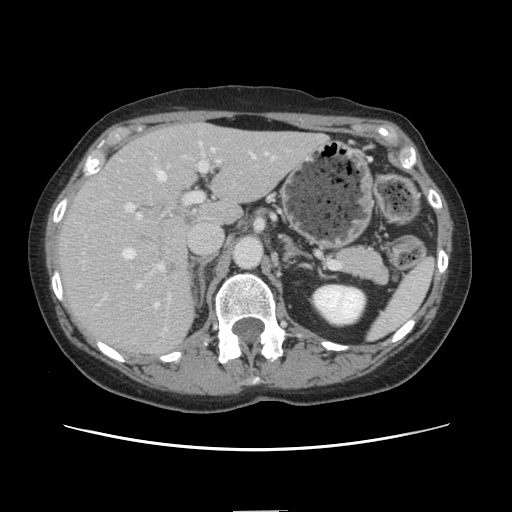
Contrast-enhanced abdominal CT, one axial slice. Slice 85 of 141 in the series (ordered by position). 120 kVp. Intravenous contrast given. Soft-tissue window (W 400 / L 40 HU). 512 × 512 image matrix. Female patient, age 63 years. From the clinical record (not read from this slice): diagnosis: colorectal cancer liver metastases, imaged before liver resection; multiple liver metastases: yes; largest metastasis: 3.2 cm; disease in both lobes: yes.
Annotated regions visible in this slice (manually delineated by an expert):
- hepatic veins: bounding box <122,149,255,308> (left, top, right, bottom; pixels)
- liver: <58,123,324,355>
- planned liver remnant (the part of the liver to remain after resection): <177,124,324,225>
- portal vein (with intrahepatic branches): <125,150,253,303>
- liver metastasis: <165,262,177,274>